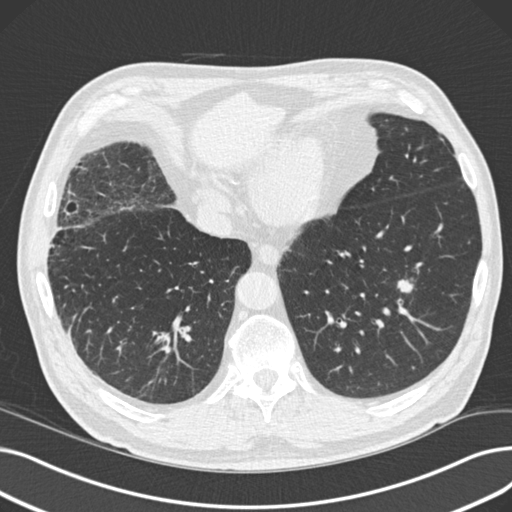
Low-dose screening chest CT, one axial slice. Position 40 of 165 along the scan axis. Reconstruction kernel B30f. 120 kVp. Lung window (W 1500 / L -600 HU). 2 mm slice thickness. 512 × 512 image matrix, field of view 369 × 369 mm.
Outlined on this slice (manually delineated by an expert):
- lesion 1 (tumor, lower lobe of left lung): bounding box [x1, y1, x2, y2] px = [397, 279, 414, 293]